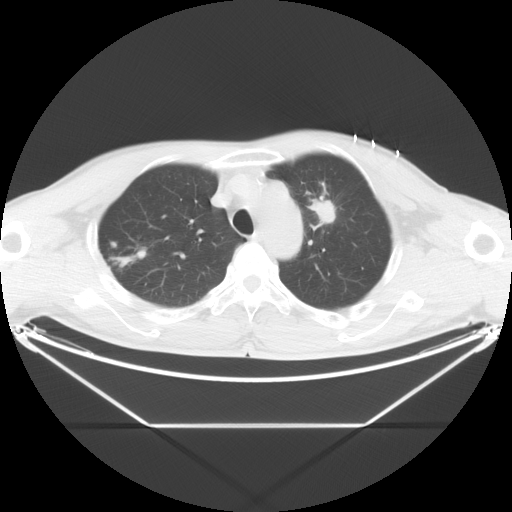
Chest CT, one axial slice; slice 21 of 26 in the series (ordered by position); reconstruction kernel STANDARD; 120 kVp; lung window (W 1500 / L -600 HU); 512 × 512 image matrix. Patient: male, 60 years. Case-level facts recorded for this patient, not image findings: clinical TNM (as recorded): T2 N1 M0.
Annotated regions visible in this slice (bounding box drawn by a radiologist):
- lung tumour (recorded histology: adenocarcinoma): bounding box [x1, y1, x2, y2] px = [308, 197, 337, 227]